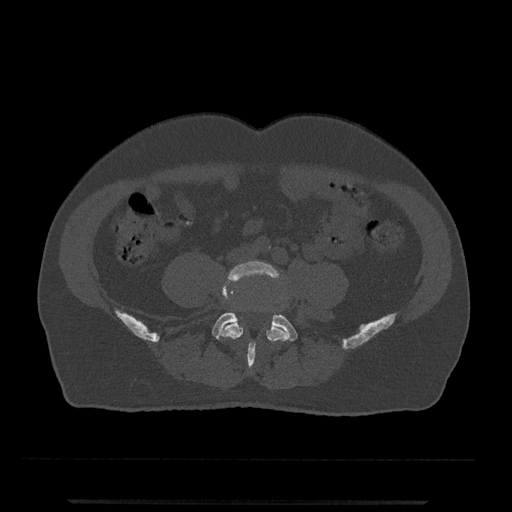
CT including the spine, one axial slice; slice 102 of 797 in the series (ordered by position); reconstruction kernel Br40s/3; 120 kVp; bone window (W 1800 / L 400 HU); 0.5 mm slice thickness; 512 × 512 image matrix. Patient: male, 63 years. Case-level facts recorded for this patient, not image findings: primary cancer: prostate.
Annotated regions visible in this slice (semi-automatic segmentation, software-assisted and operator-edited):
- L4 vertebra: bounding box (x1, y1, x2, y2) in pixels: (220, 261, 289, 367)
- L5 vertebra: (212, 312, 298, 360)